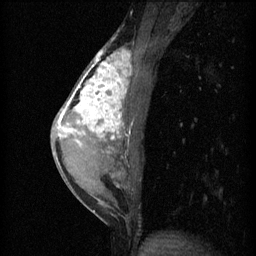
Breast MRI (dynamic contrast-enhanced), one sagittal slice. Position 28 of 60 along the scan axis. 3 images stored at this slice position (order not interpretable as contrast timing). 1.5 T. TE 4.2 ms, TR 11 ms. 2 mm slice thickness. 256 × 256 image matrix, field of view 180 × 180 mm. Patient: female, 40 years.
Outlined on this slice (semi-automatically segmented with operator editing):
- analysis volume of interest (the breast-tissue region the enhancement analysis was run in; not a lesion): bounding box (x1, y1, x2, y2) in pixels: (55, 42, 142, 203)
- tumour enhancement mask (voxels above the 70 % enhancement threshold inside the analysis volume of interest): (58, 50, 133, 151)